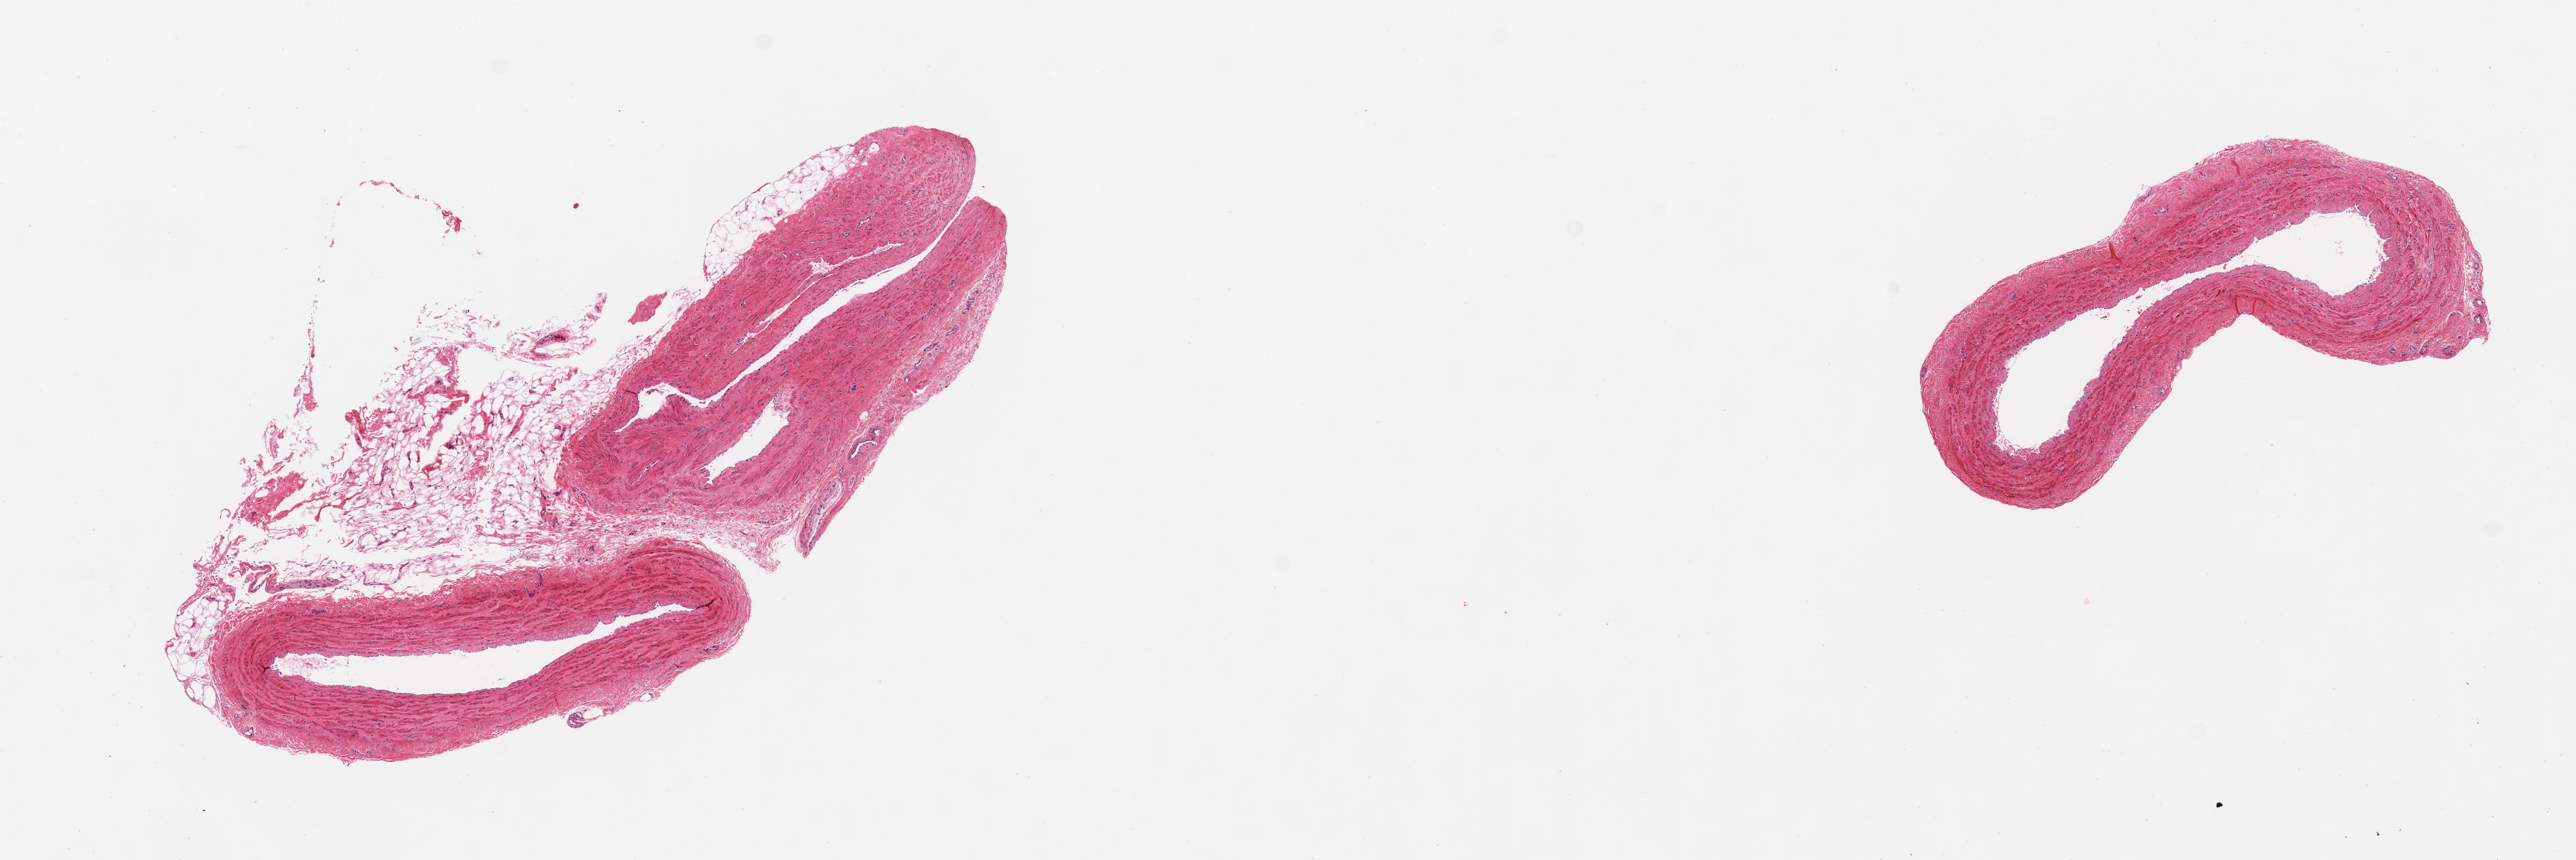
Digitized haematoxylin and eosin-stained section, low-resolution overview of the scanned area, about 14.8 x 4.9 mm (slide scanned at 20x). PAXgene-fixed paraffin-embedded (PFPE) section. Target tissue: tibial nerve. Donor tissue sample.
Pathologist's review note for this sample: 2 pieces; vessels and fat, not nerve.